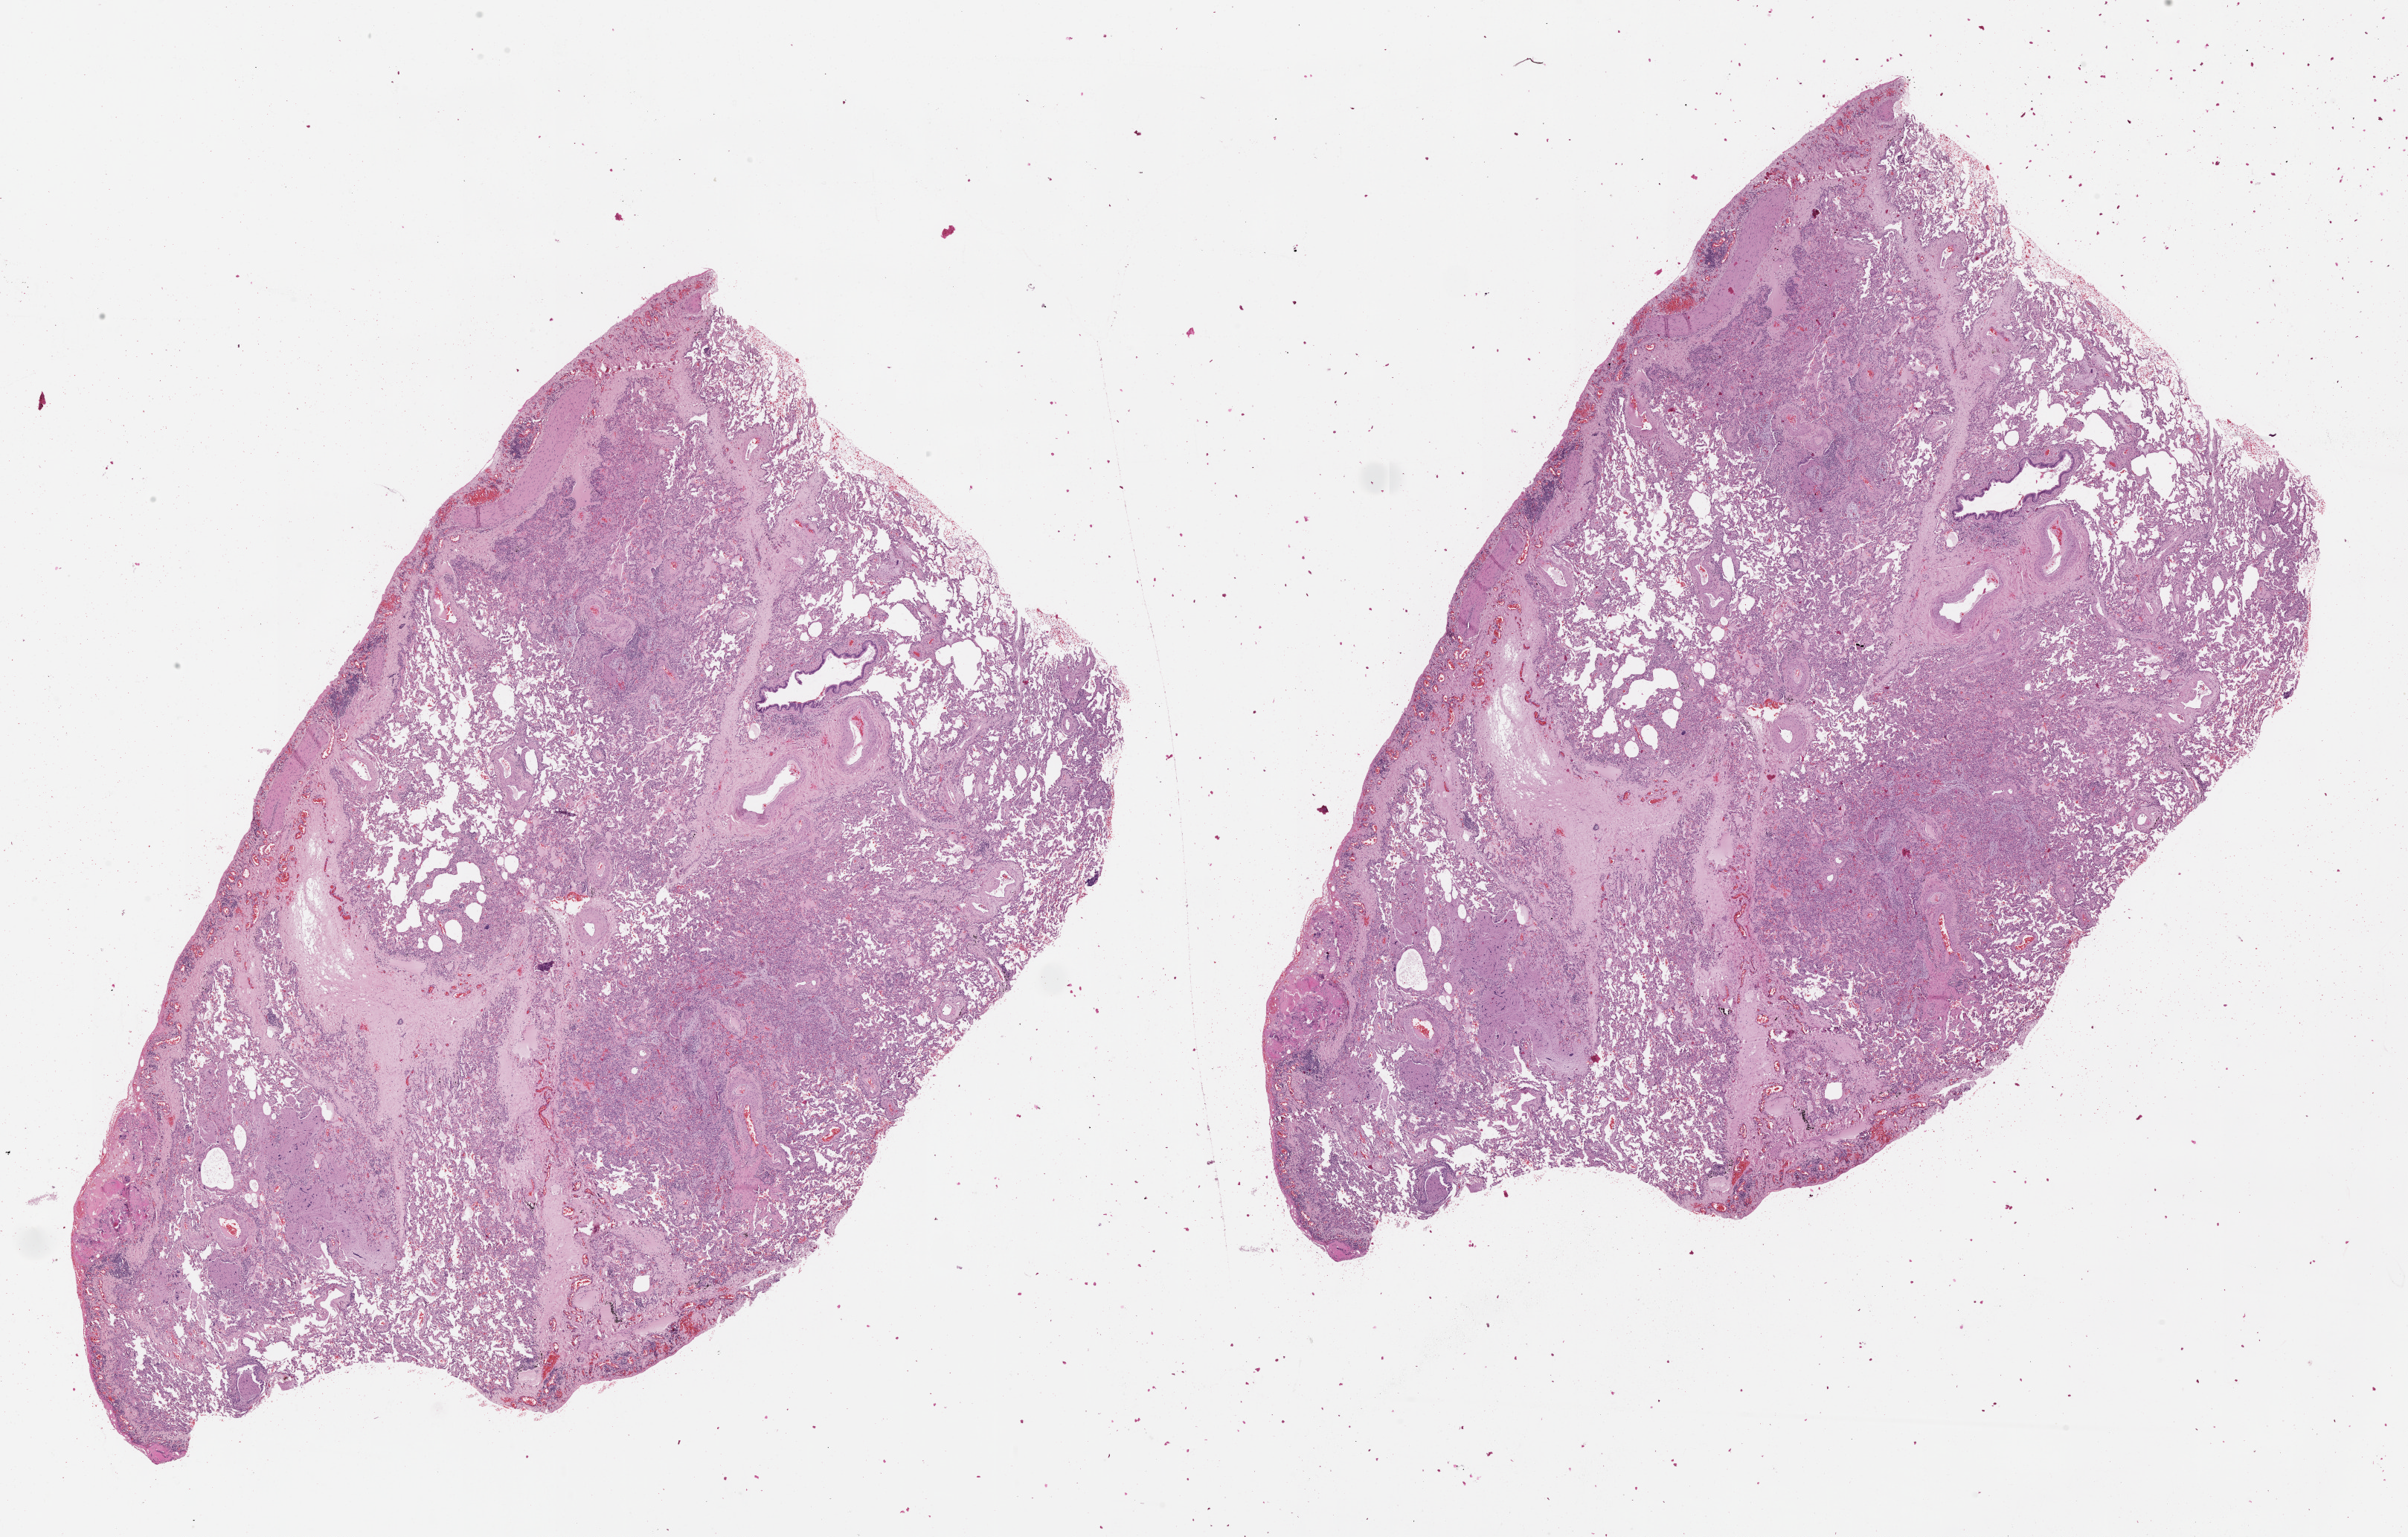
Digitized H&E-stained tissue section (whole slide), a low-resolution overview of the entire scanned area, about 26.1 x 16.6 mm (from a 20x scan). Lung, normal (non-tumour) tissue. Patient: male, age 69 years.
This section: normal (non-tumour) tissue from the same patient. Patient diagnosis (cohort enrolment): squamous cell carcinoma (lung).